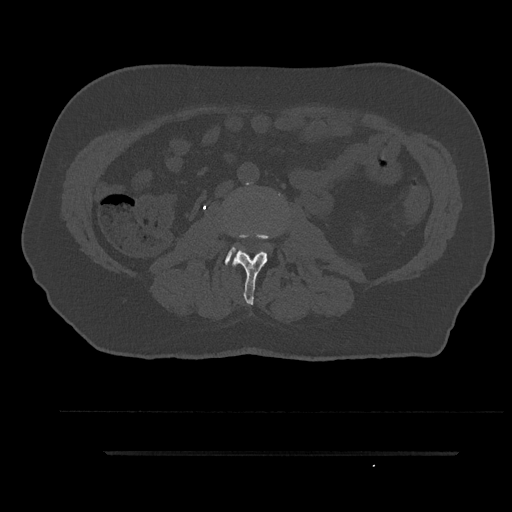
CT including the spine, one axial slice. Slice 81 of 797 in the series (ordered by position). 120 kVp. Bone window (W 1800 / L 400 HU). 0.5 mm slice thickness. 512 × 512 image matrix, field of view 432 × 432 mm. Male patient, age 63 years. Case-level facts recorded for this patient, not image findings: primary cancer: renal.
Structures marked on this image (semi-automatic segmentation, software-assisted and operator-edited):
- L2 vertebra: bounding box (x1, y1, x2, y2) in pixels: (232, 233, 278, 305)
- L3 vertebra: (225, 246, 268, 265)